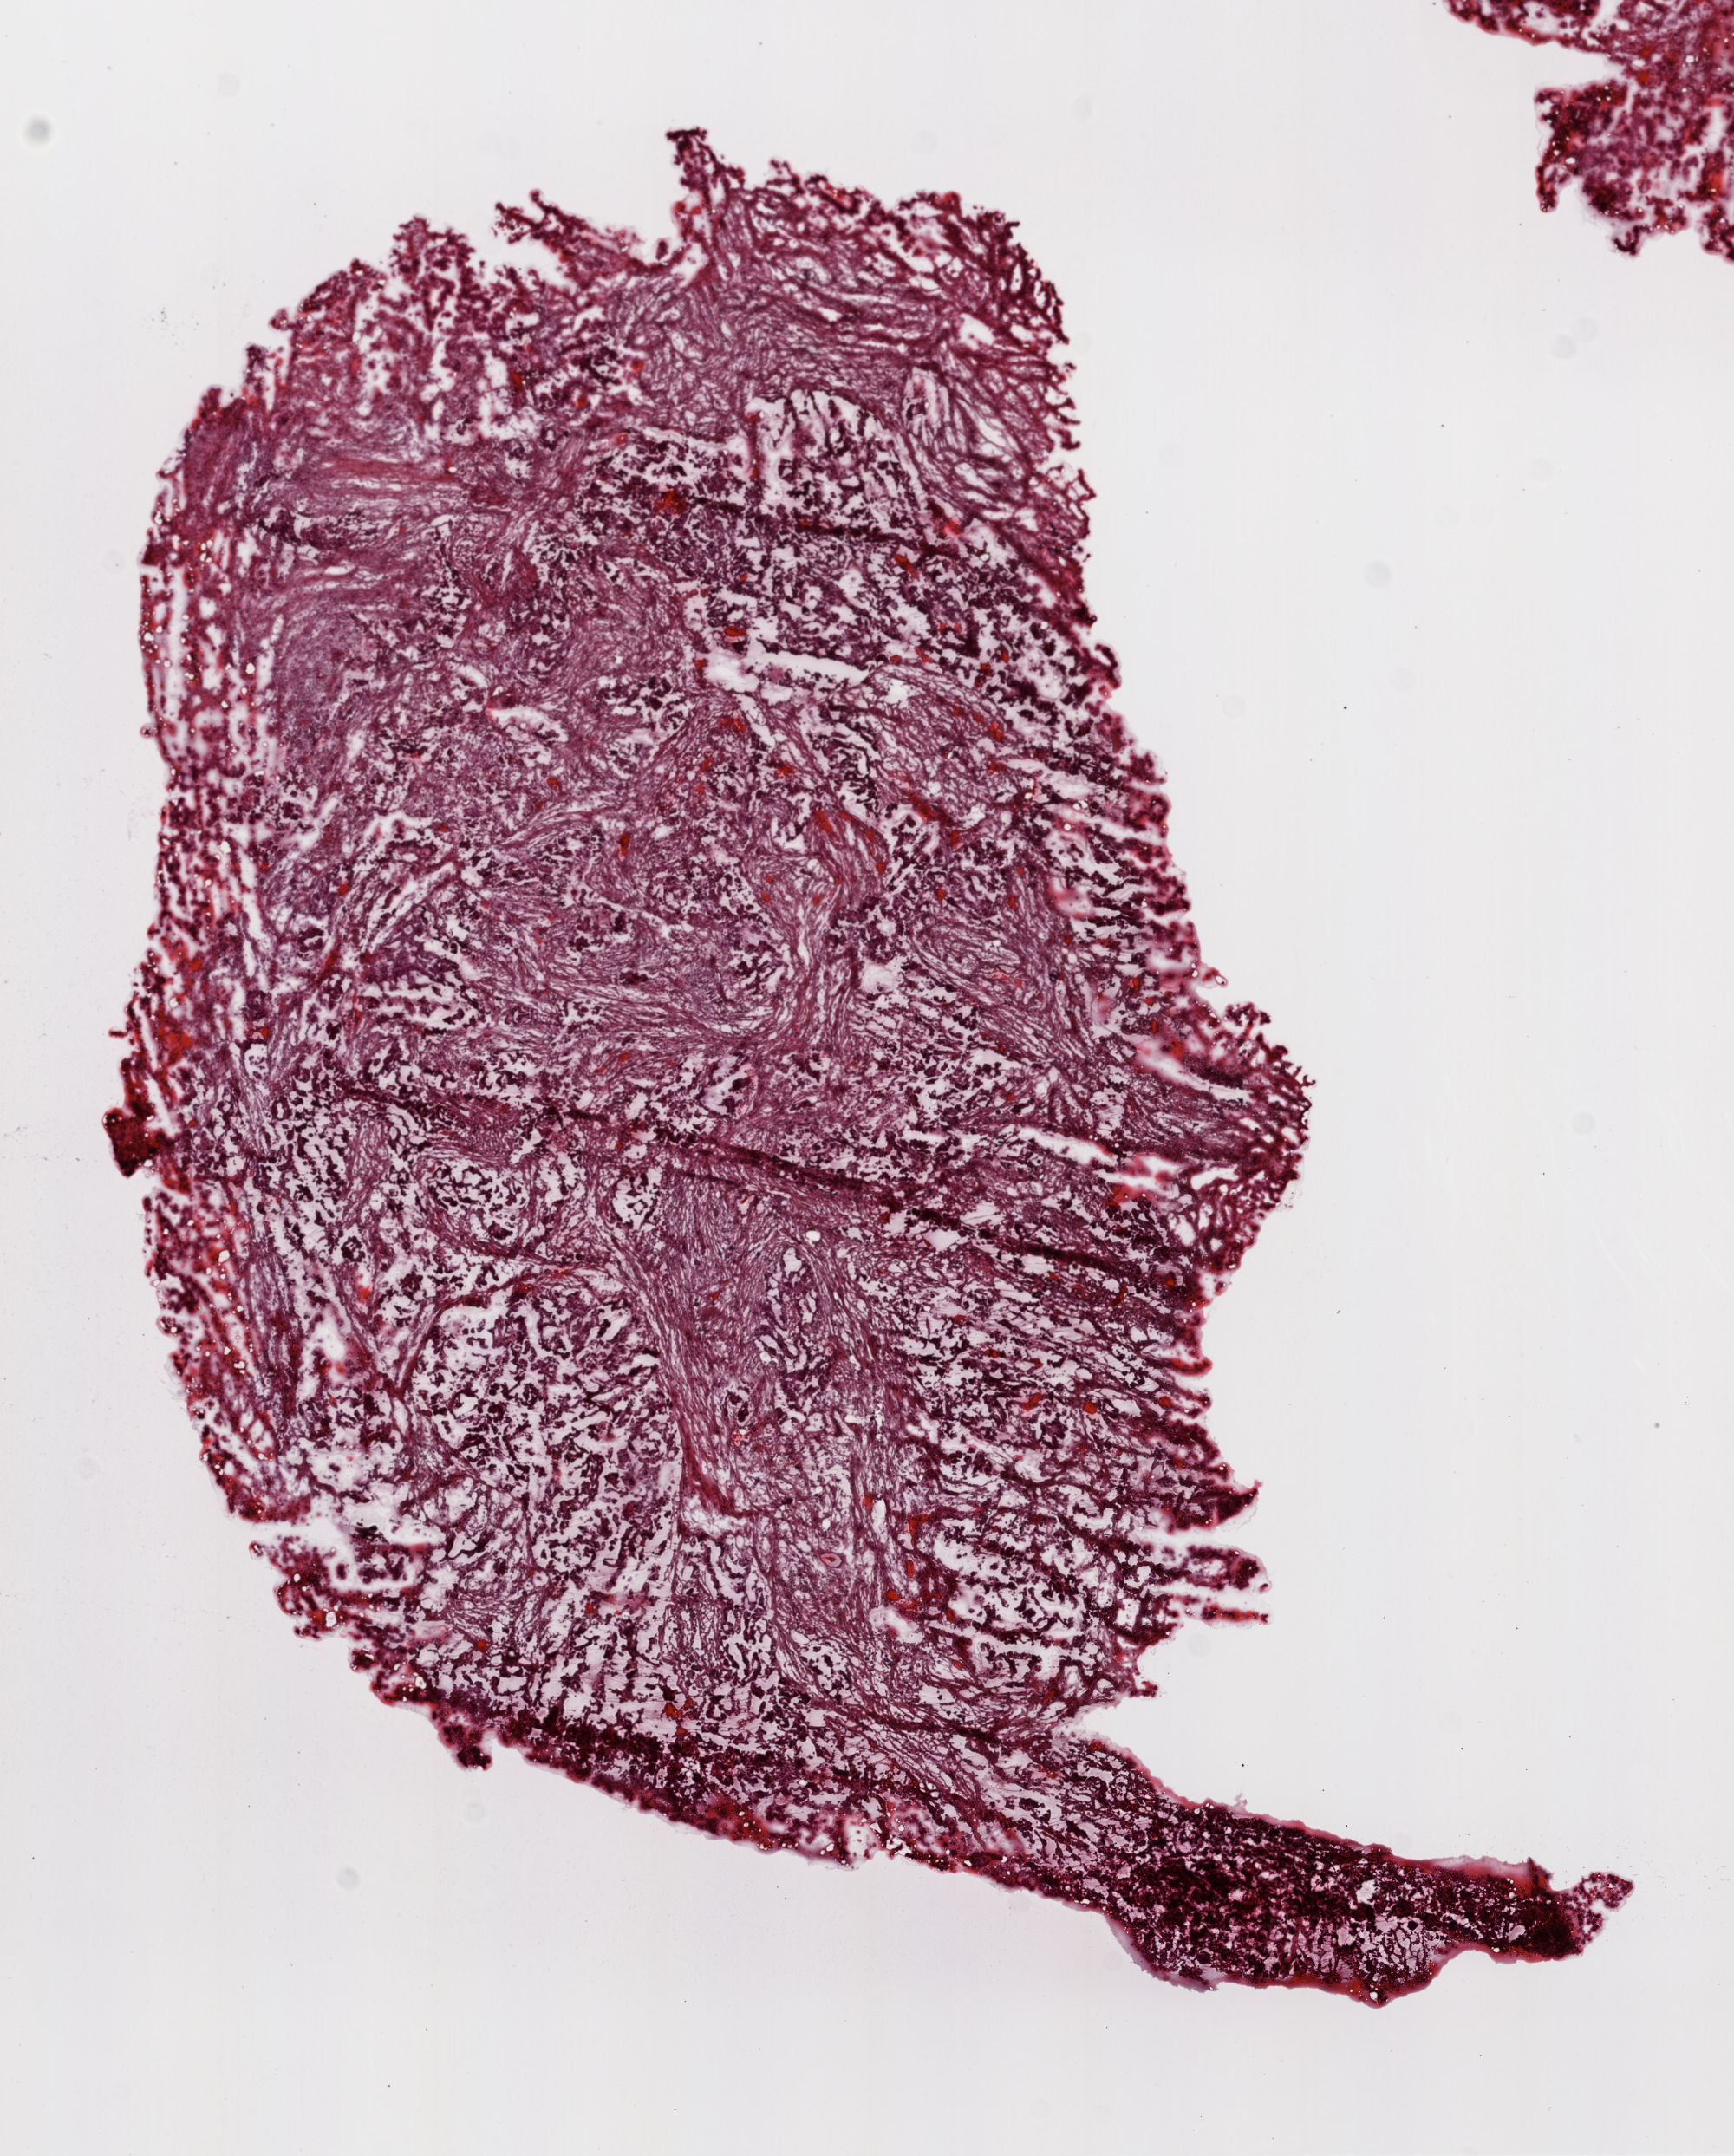
H&E whole-slide image — low-resolution overview of the scanned area, about 8.0 x 10.0 mm (from a 20x scan), frozen section from the top of the tissue portion, primary tumour sample from the ovary. Female, age 75 years at initial diagnosis. Histologic grade: G3 (poorly differentiated). Slide review estimates, as recorded: tumour cells 80%, tumour nuclei 80%, normal cells 0%, stromal cells 20%, necrosis 0%. Inflammatory infiltration, as recorded: lymphocyte infiltration 0%, monocyte infiltration 0%, neutrophil infiltration 0%.
* FIGO stage: IIIC
* laterality: bilateral
* pathologic diagnosis: Serous cystadenocarcinoma, NOS